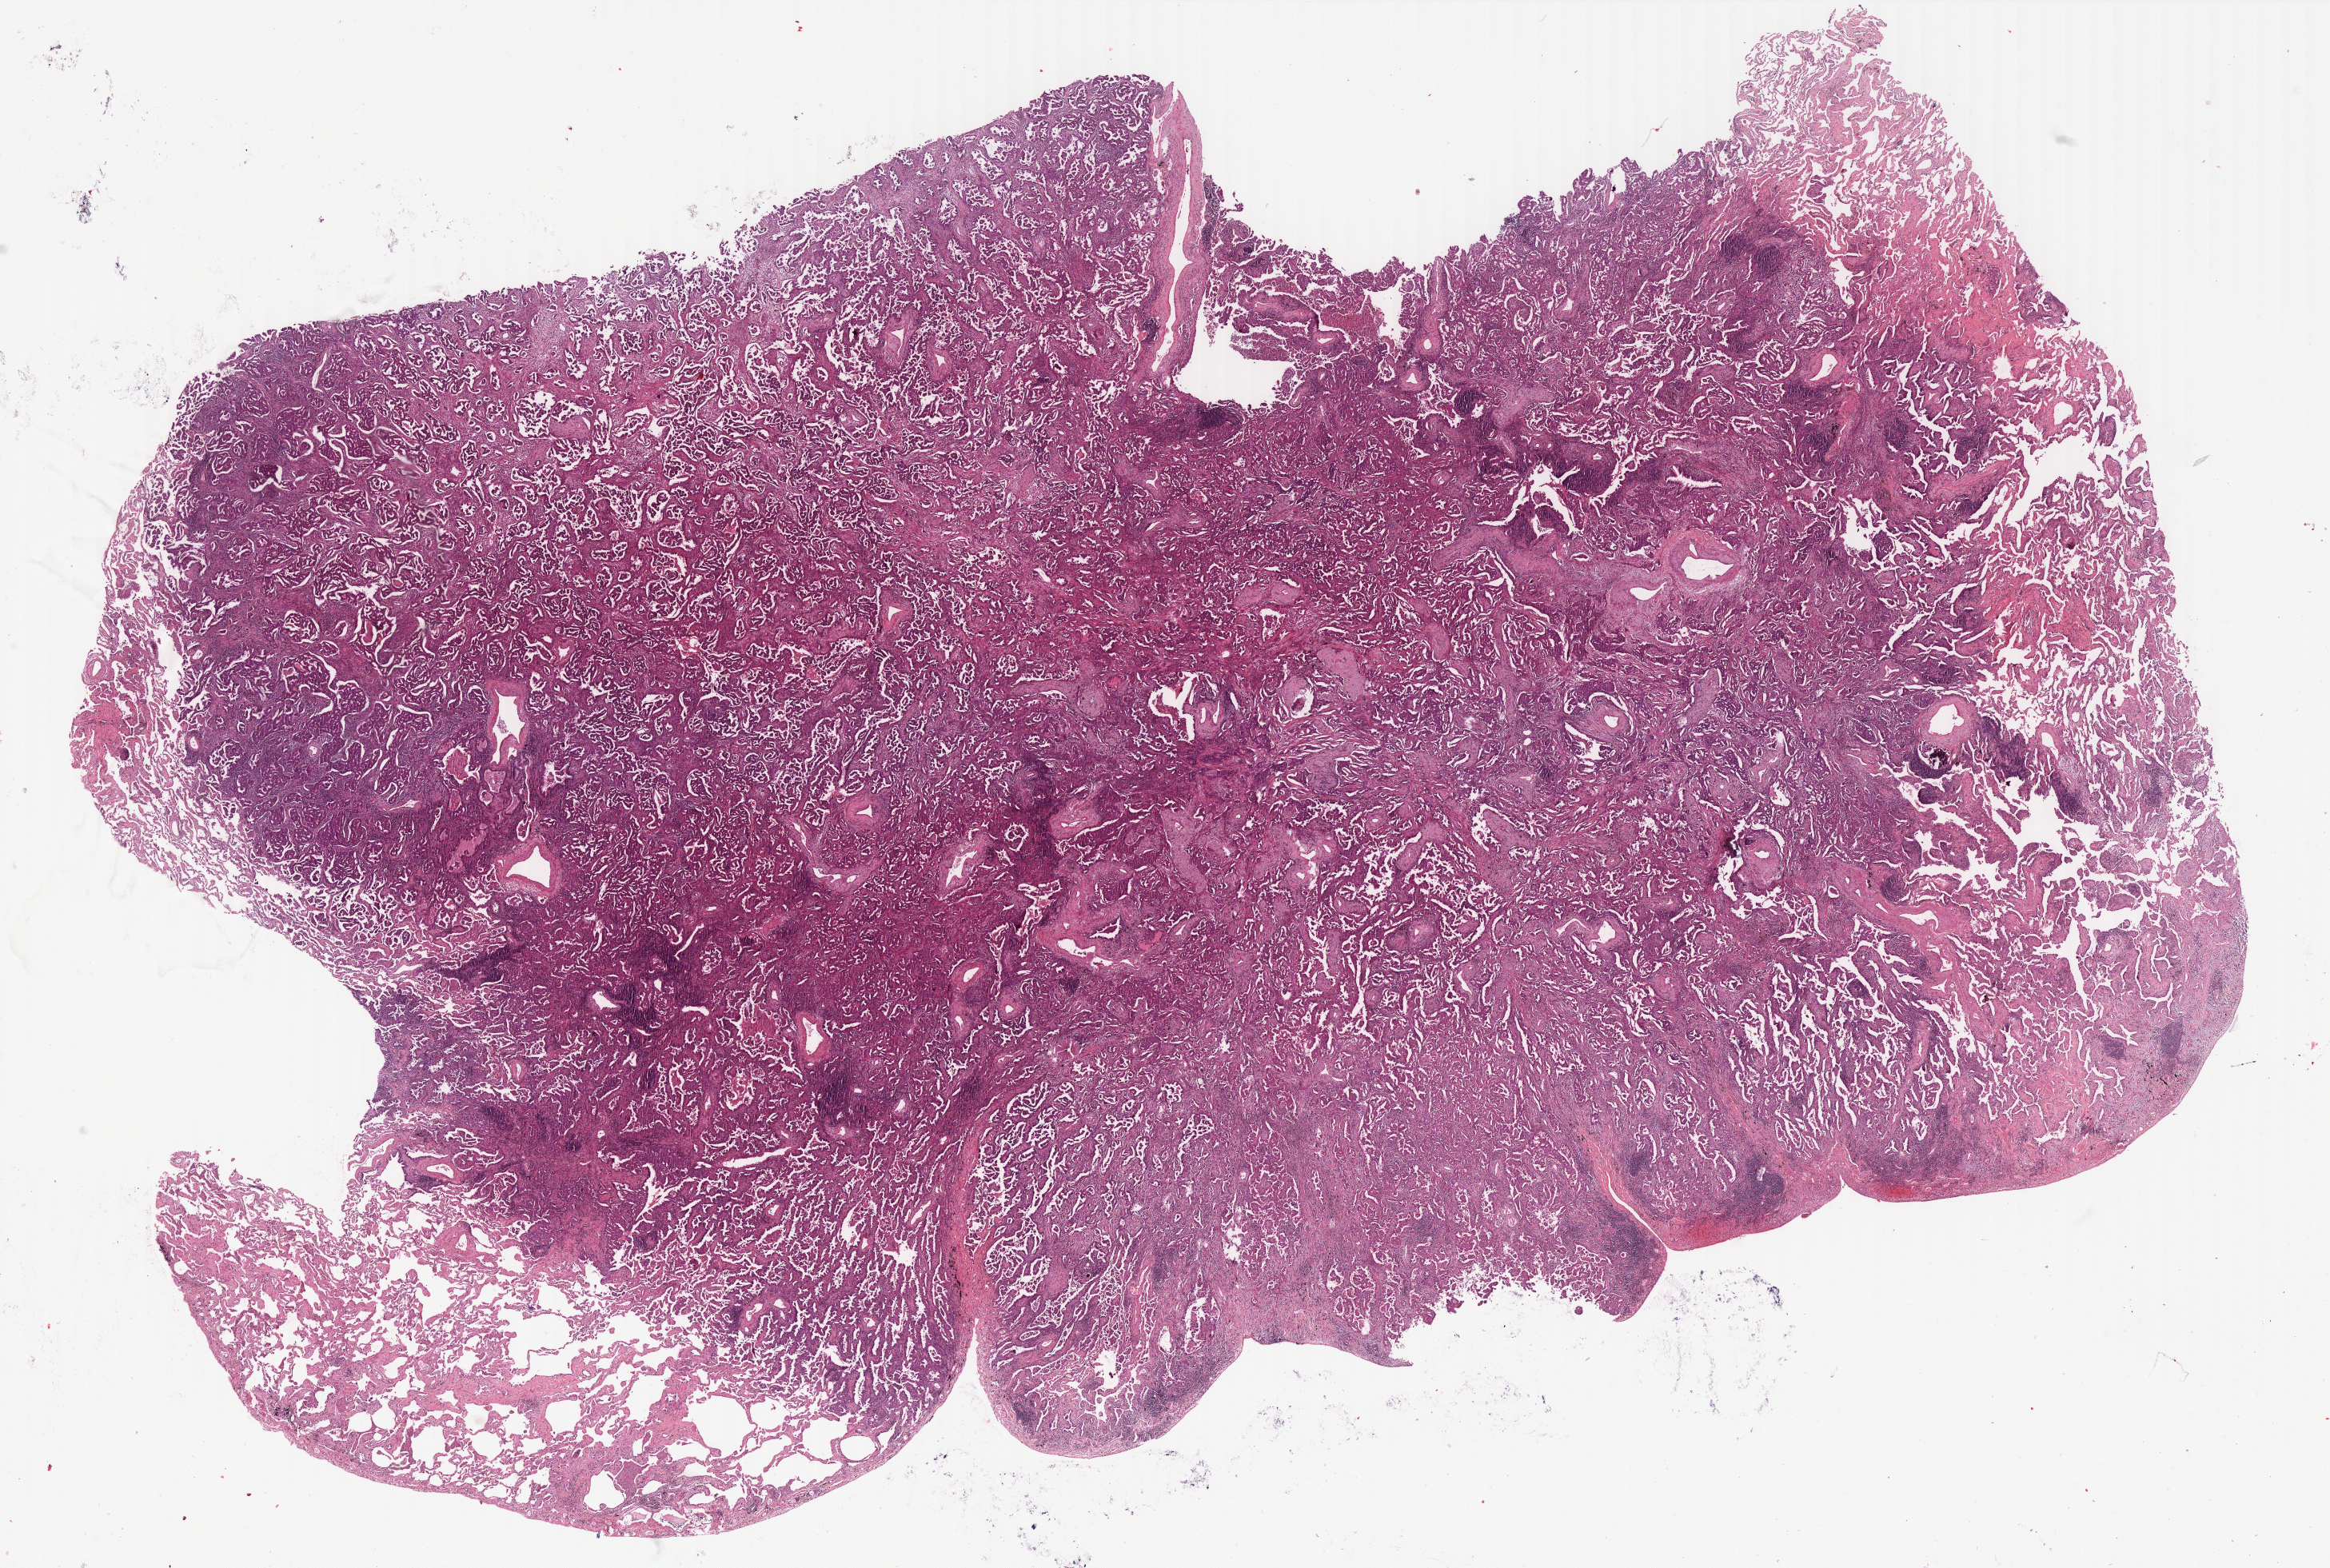
Whole-slide histology image, H&E-stained, low-resolution overview of the scanned area, about 23.5 x 15.8 mm (from a 40x scan); formalin-fixed paraffin-embedded (FFPE) diagnostic section; lung, primary tumour sample. Male, age 70 years at initial diagnosis.
AJCC pathologic stage: IIB (7th edition). Diagnosis: Adenocarcinoma, NOS (lower lobe, lung).